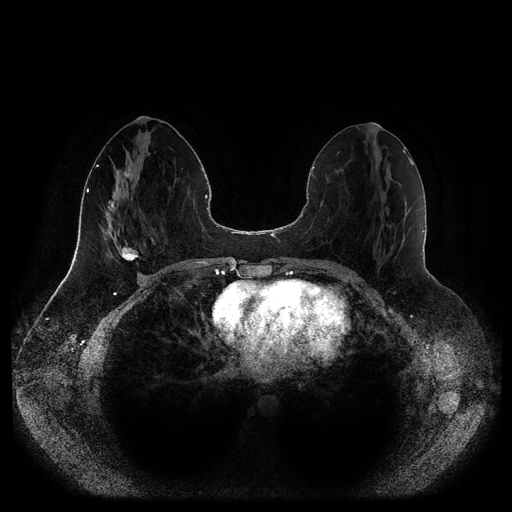
Breast MRI (dynamic contrast-enhanced, multi-phase), one axial slice. Position 44 of 116 along the scan axis. Dynamic contrast-enhanced series, time point 2 of 5 at this slice position (early post-contrast). 1.5 T. TE 2.5 ms, TR 5.2 ms. 2 mm slice thickness. 512 × 512 image matrix, field of view 390 × 390 mm. Patient: female, 44 years.
Annotated regions visible in this slice (semi-automatic segmentation, software-assisted and operator-edited):
- breast lesion (labelled 'tumour' in the annotation; benign lesions carry a separate 'benign' label): bounding box [x1, y1, x2, y2] px = [120, 245, 139, 263]